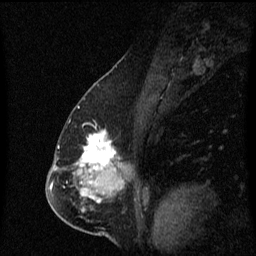
Breast MRI (dynamic contrast-enhanced), one sagittal slice. Position 35 of 60 along the scan axis. Dynamic contrast-enhanced series, image 2 of 3 at this slice position (ordered by acquisition). 1.5 T. TE 4.2 ms, TR 8.4 ms. 2 mm slice thickness. 256 × 256 image matrix. Female patient, age 57 years. Case-level facts recorded for this patient, not image findings: setting: breast cancer imaged before/during neoadjuvant chemotherapy; receptor status: HR-positive, HER2-negative.
Outlined on this slice (semi-automatically segmented with operator editing):
- analysis volume of interest (the breast-tissue region the enhancement analysis was run in; not a lesion): bounding box (x1, y1, x2, y2) in pixels: (73, 130, 129, 177)
- tumour enhancement mask (voxels above the 70 % enhancement threshold inside the analysis volume of interest): (80, 130, 116, 171)